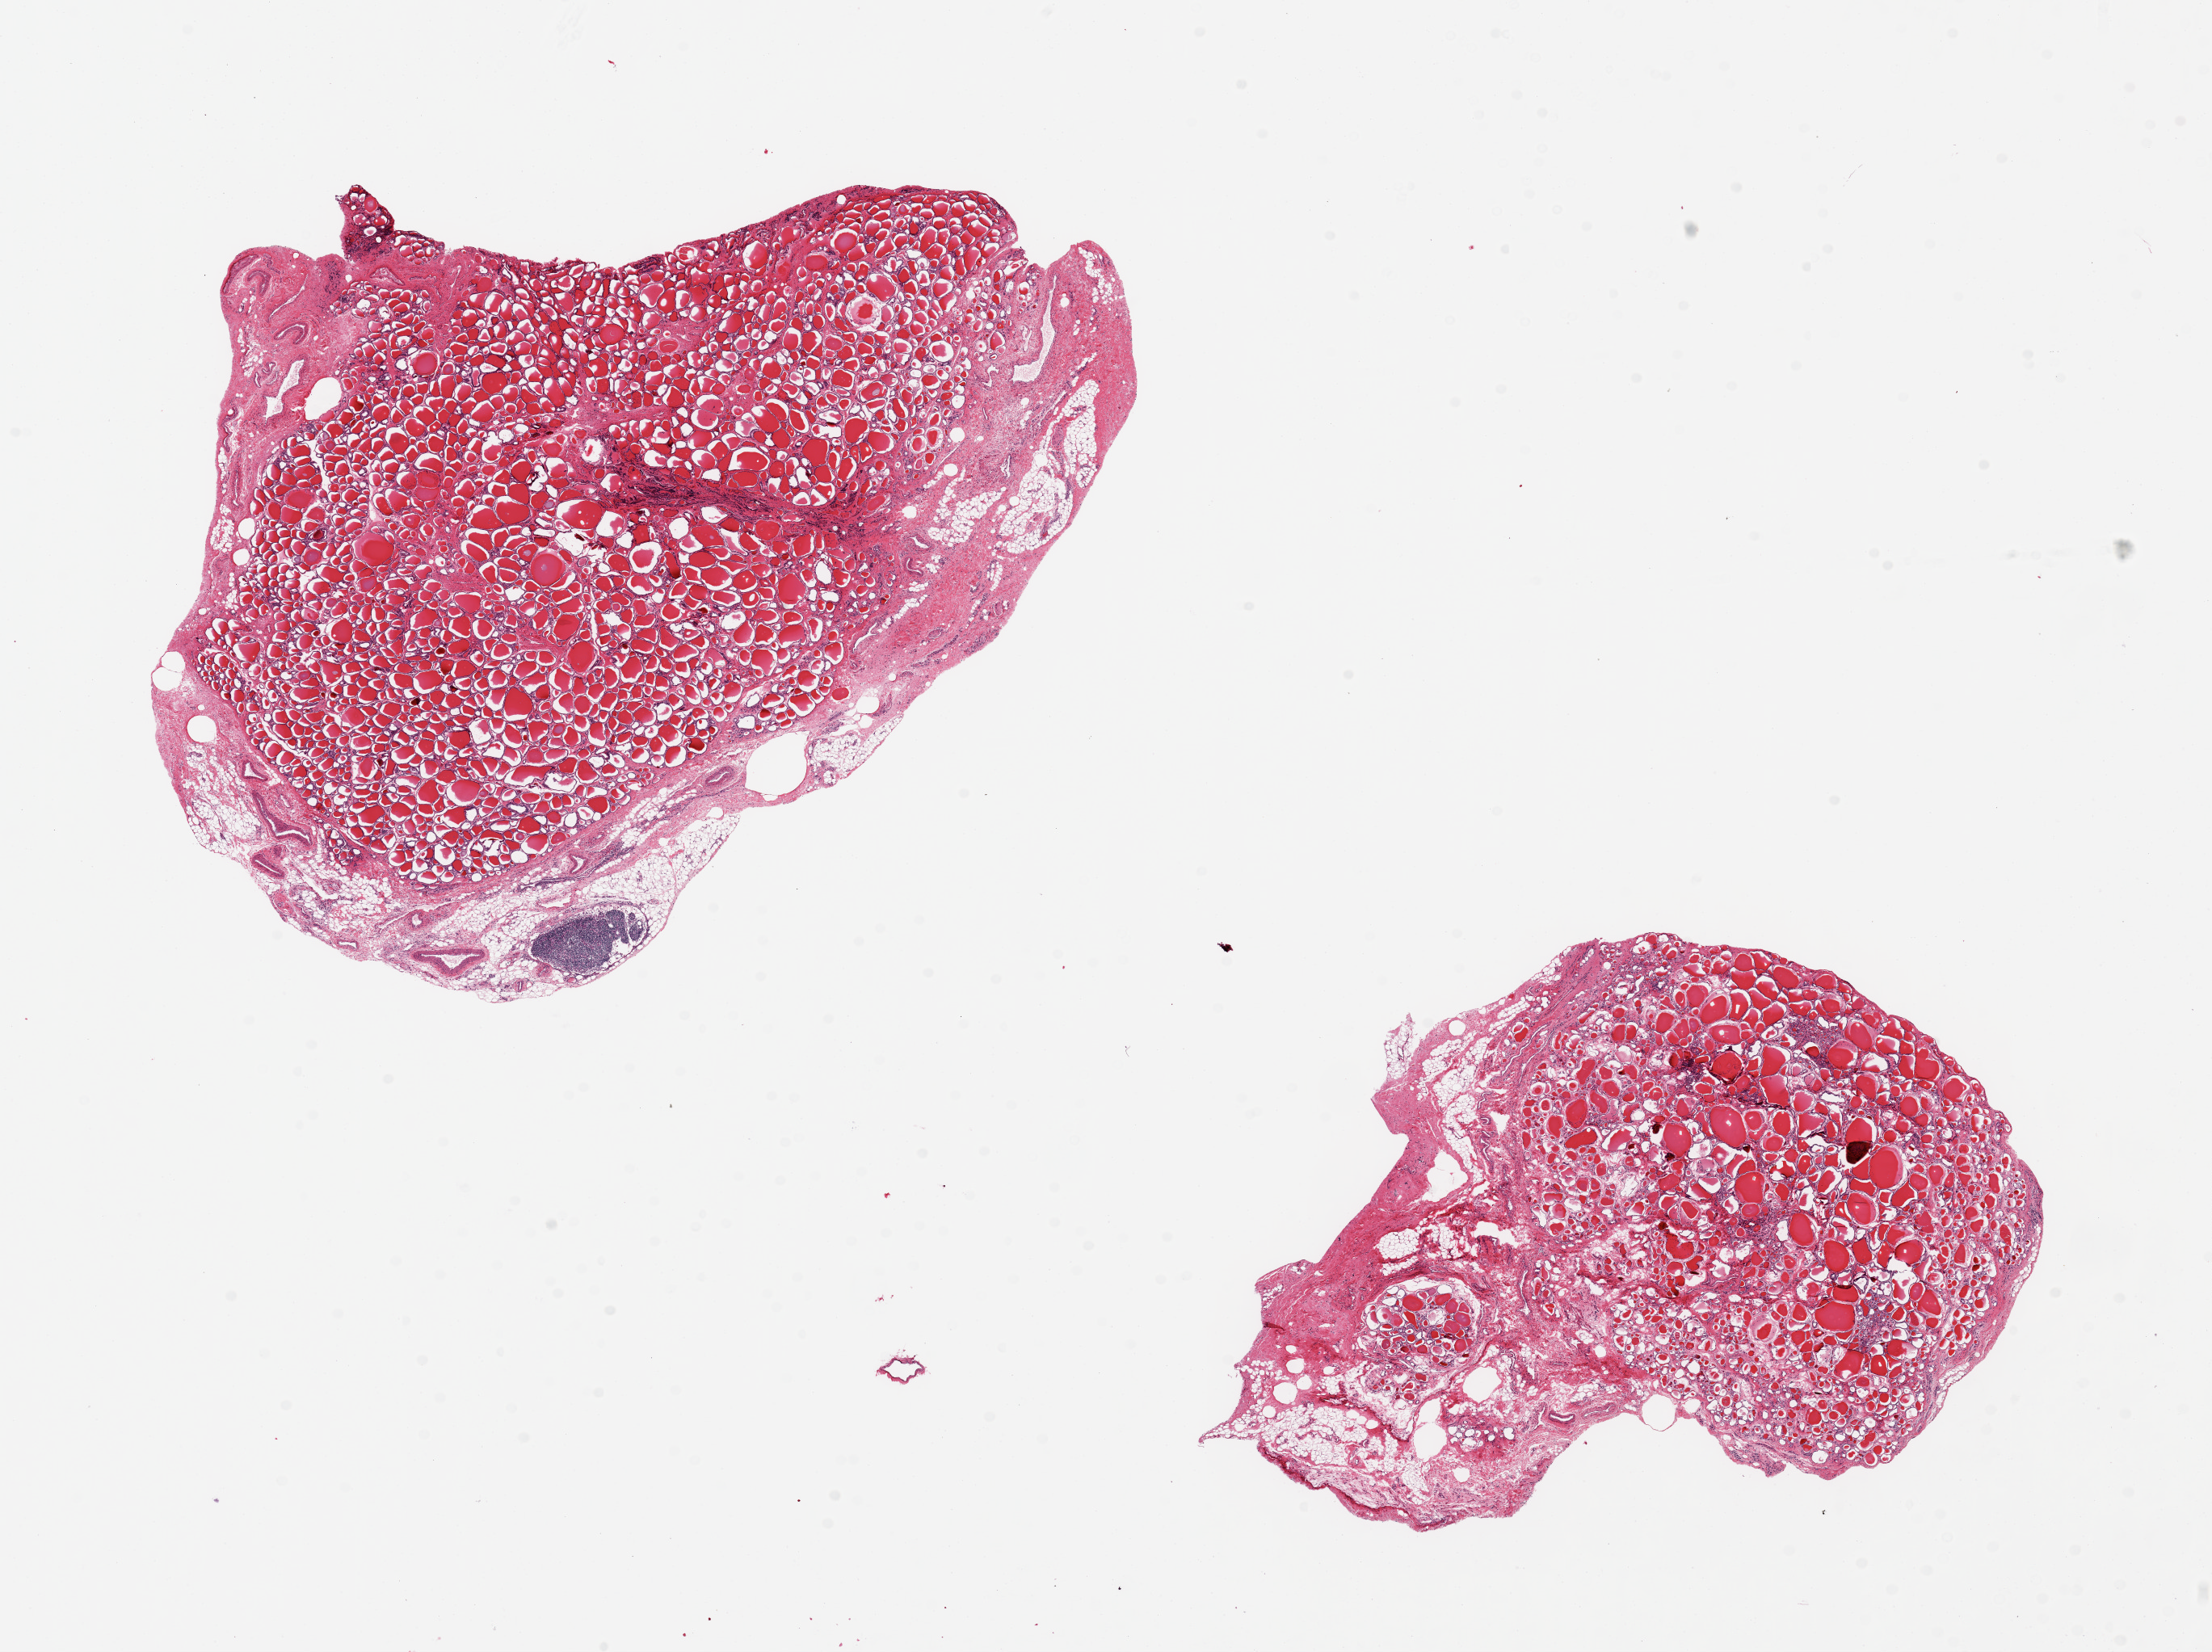
Digitized H&E-stained section, brightfield — low-resolution overview of the scanned area, about 21.7 x 16.2 mm (slide scanned at 20x), PAXgene-fixed, paraffin-embedded tissue, target tissue: thyroid, donor tissue sample.
Pathologist's review note for this sample: 2 pieces, 10x9 & 7x5mm; 10-20% peripheral adipose and stroma.